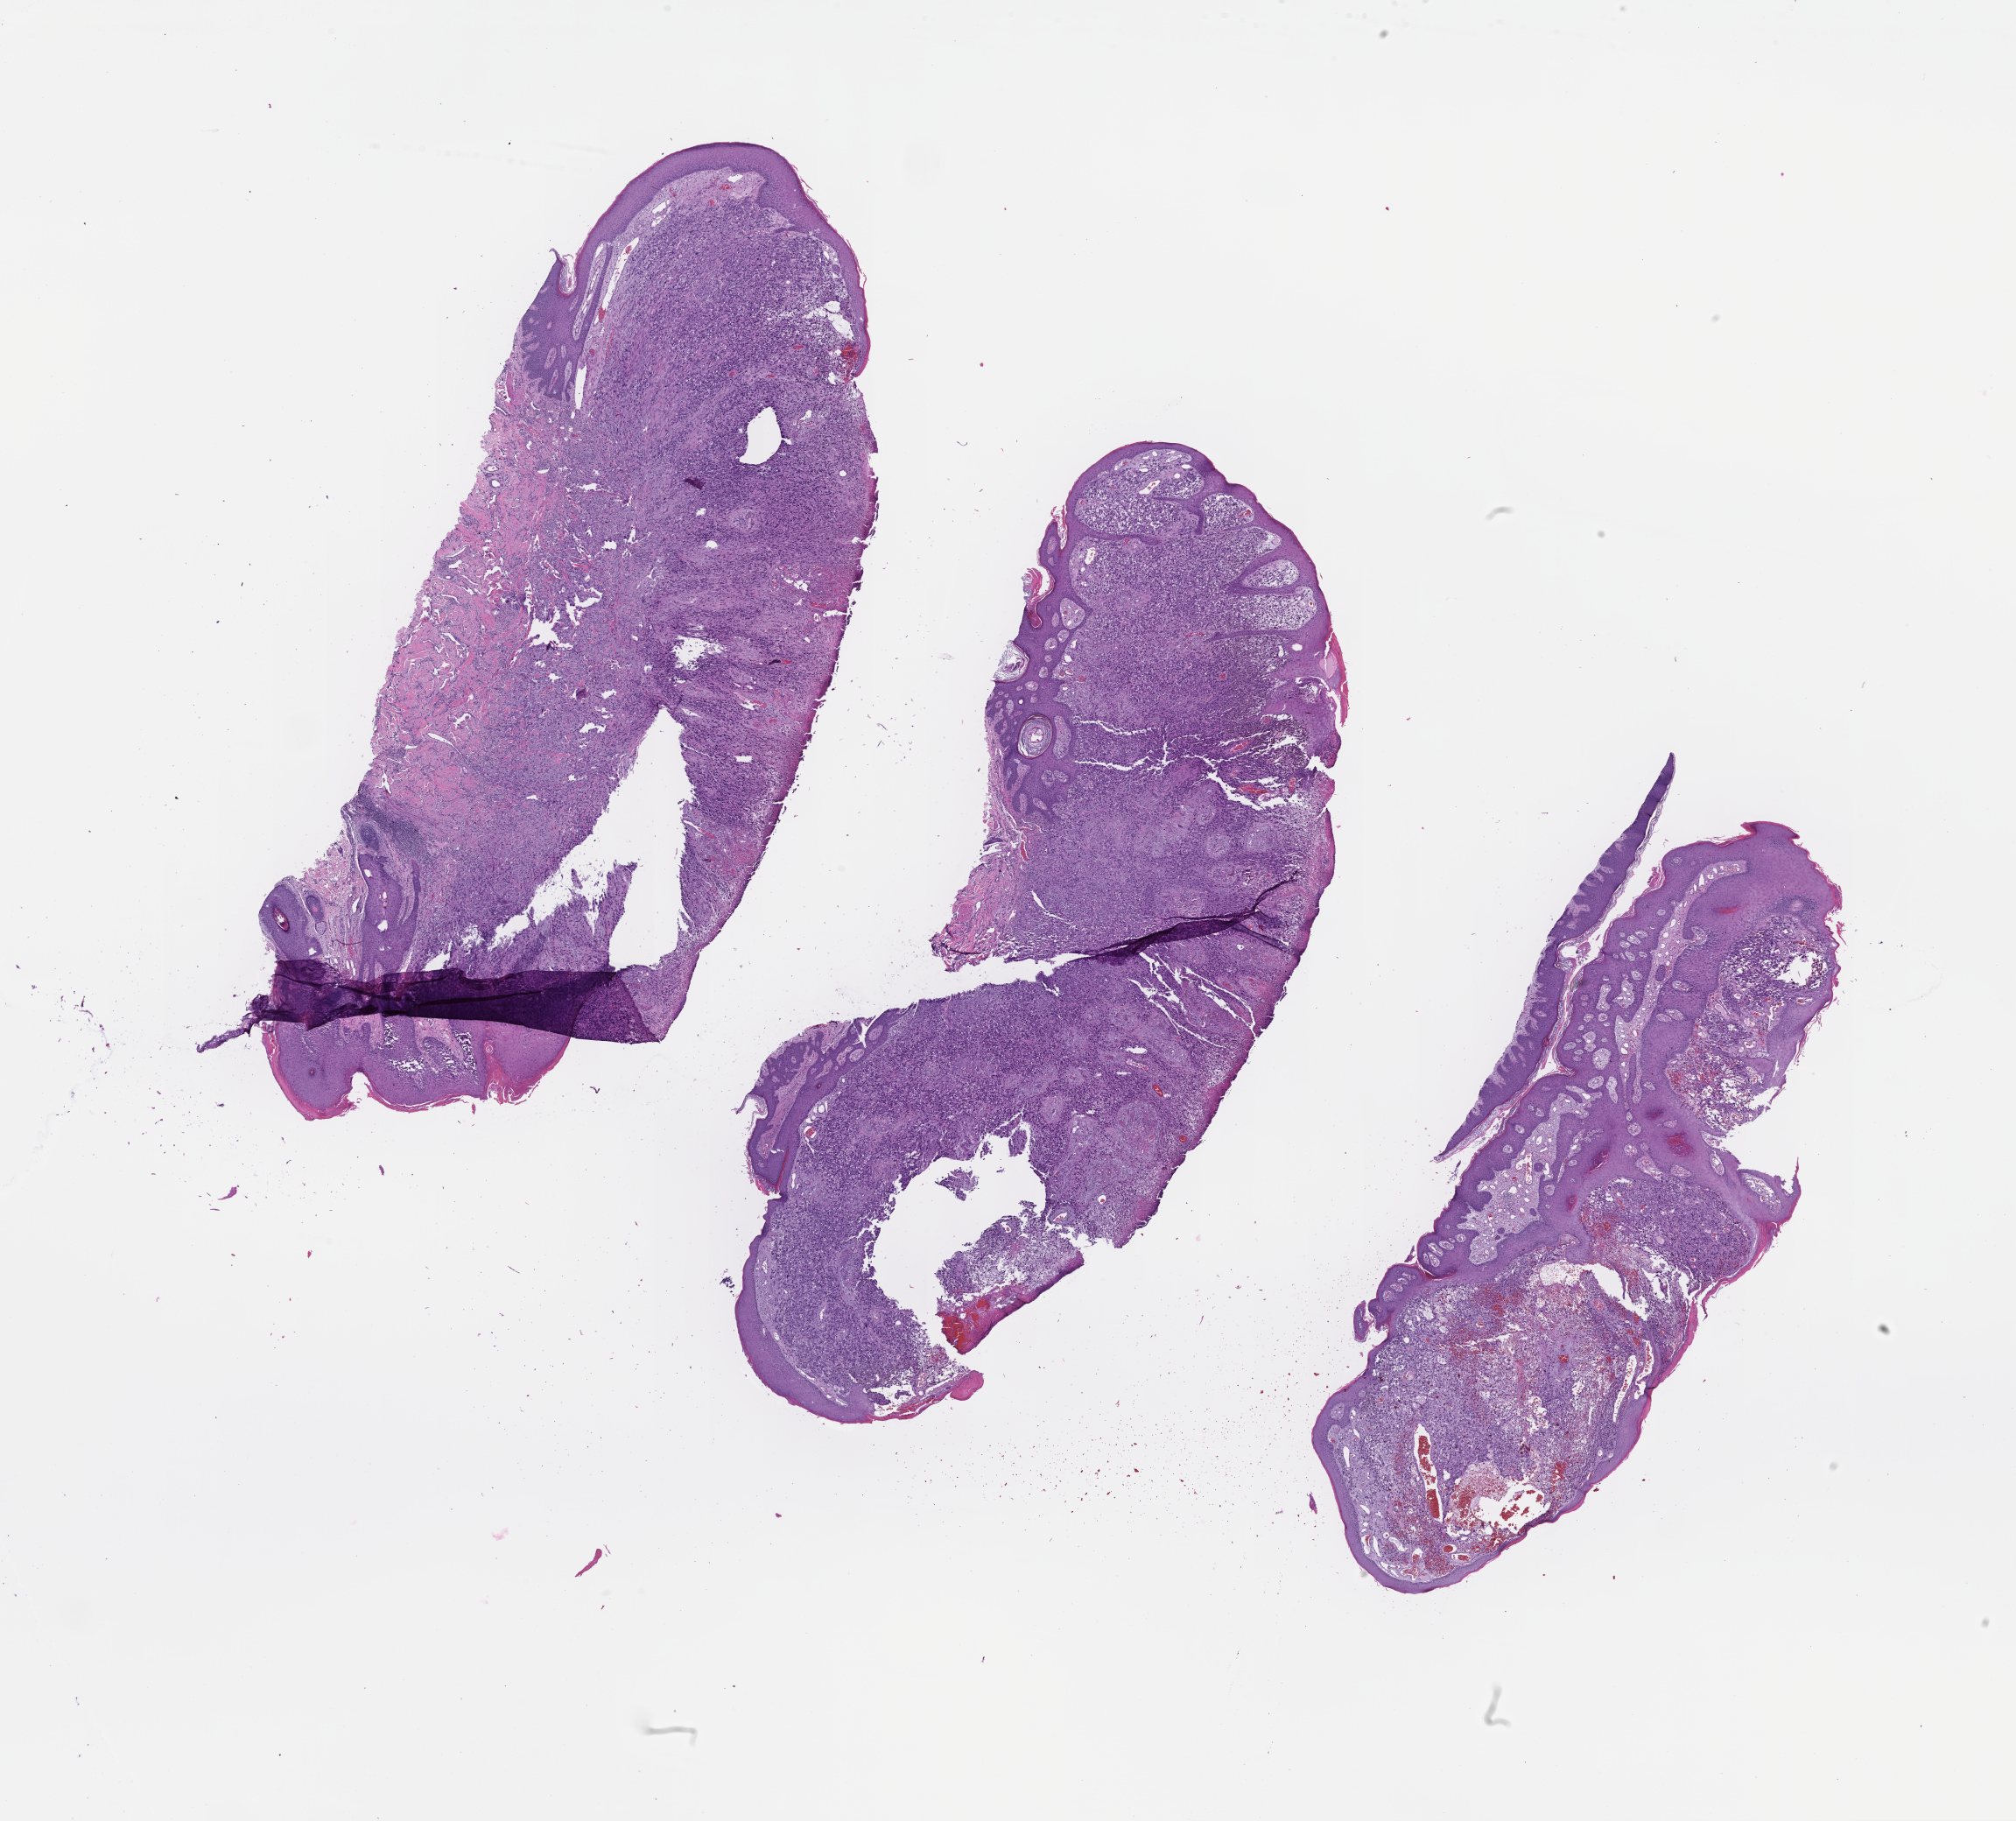
Digitized H&E-stained section — shown as a low-resolution overview of the whole scanned area (about 18.6 x 16.8 mm); formalin-fixed paraffin-embedded section; tissue site: skin; specimen time point: archival tissue. Patient sex: male.
This section: primary tumor. Diagnosis: Melanoma.